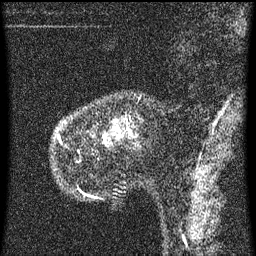
Breast MRI (dynamic contrast-enhanced), one sagittal slice. Slice 15 of 60 in the series (ordered by position). Dynamic contrast-enhanced series, image 2 of 3 at this slice position (ordered by acquisition). 1.5 T. TE 4.2 ms, TR 8 ms. 2 mm slice thickness. 256 × 256 image matrix. Patient: female, 55 years.
Structures marked on this image (semi-automatic segmentation, software-assisted and operator-edited):
- analysis volume of interest (the breast-tissue region the enhancement analysis was run in; not a lesion): bounding box [x1, y1, x2, y2] px = [55, 96, 140, 153]
- tumour enhancement mask (voxels above the 70 % enhancement threshold inside the analysis volume of interest): [59, 130, 121, 141]